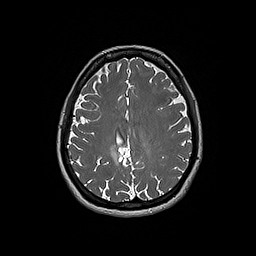
Brain MRI from a brain-tumour surgery series, one axial slice; slice 69 of 192 in the series (ordered by position); 256 × 256 image matrix, field of view 250 × 250 mm. From the clinical record (not read from this slice): histopathology: Oligodendroglioma; WHO grade: 2; IDH mutation: yes.
Annotated regions visible in this slice (outlined manually by an expert reader):
- tumour: bounding box <110,144,124,165> (left, top, right, bottom; pixels)